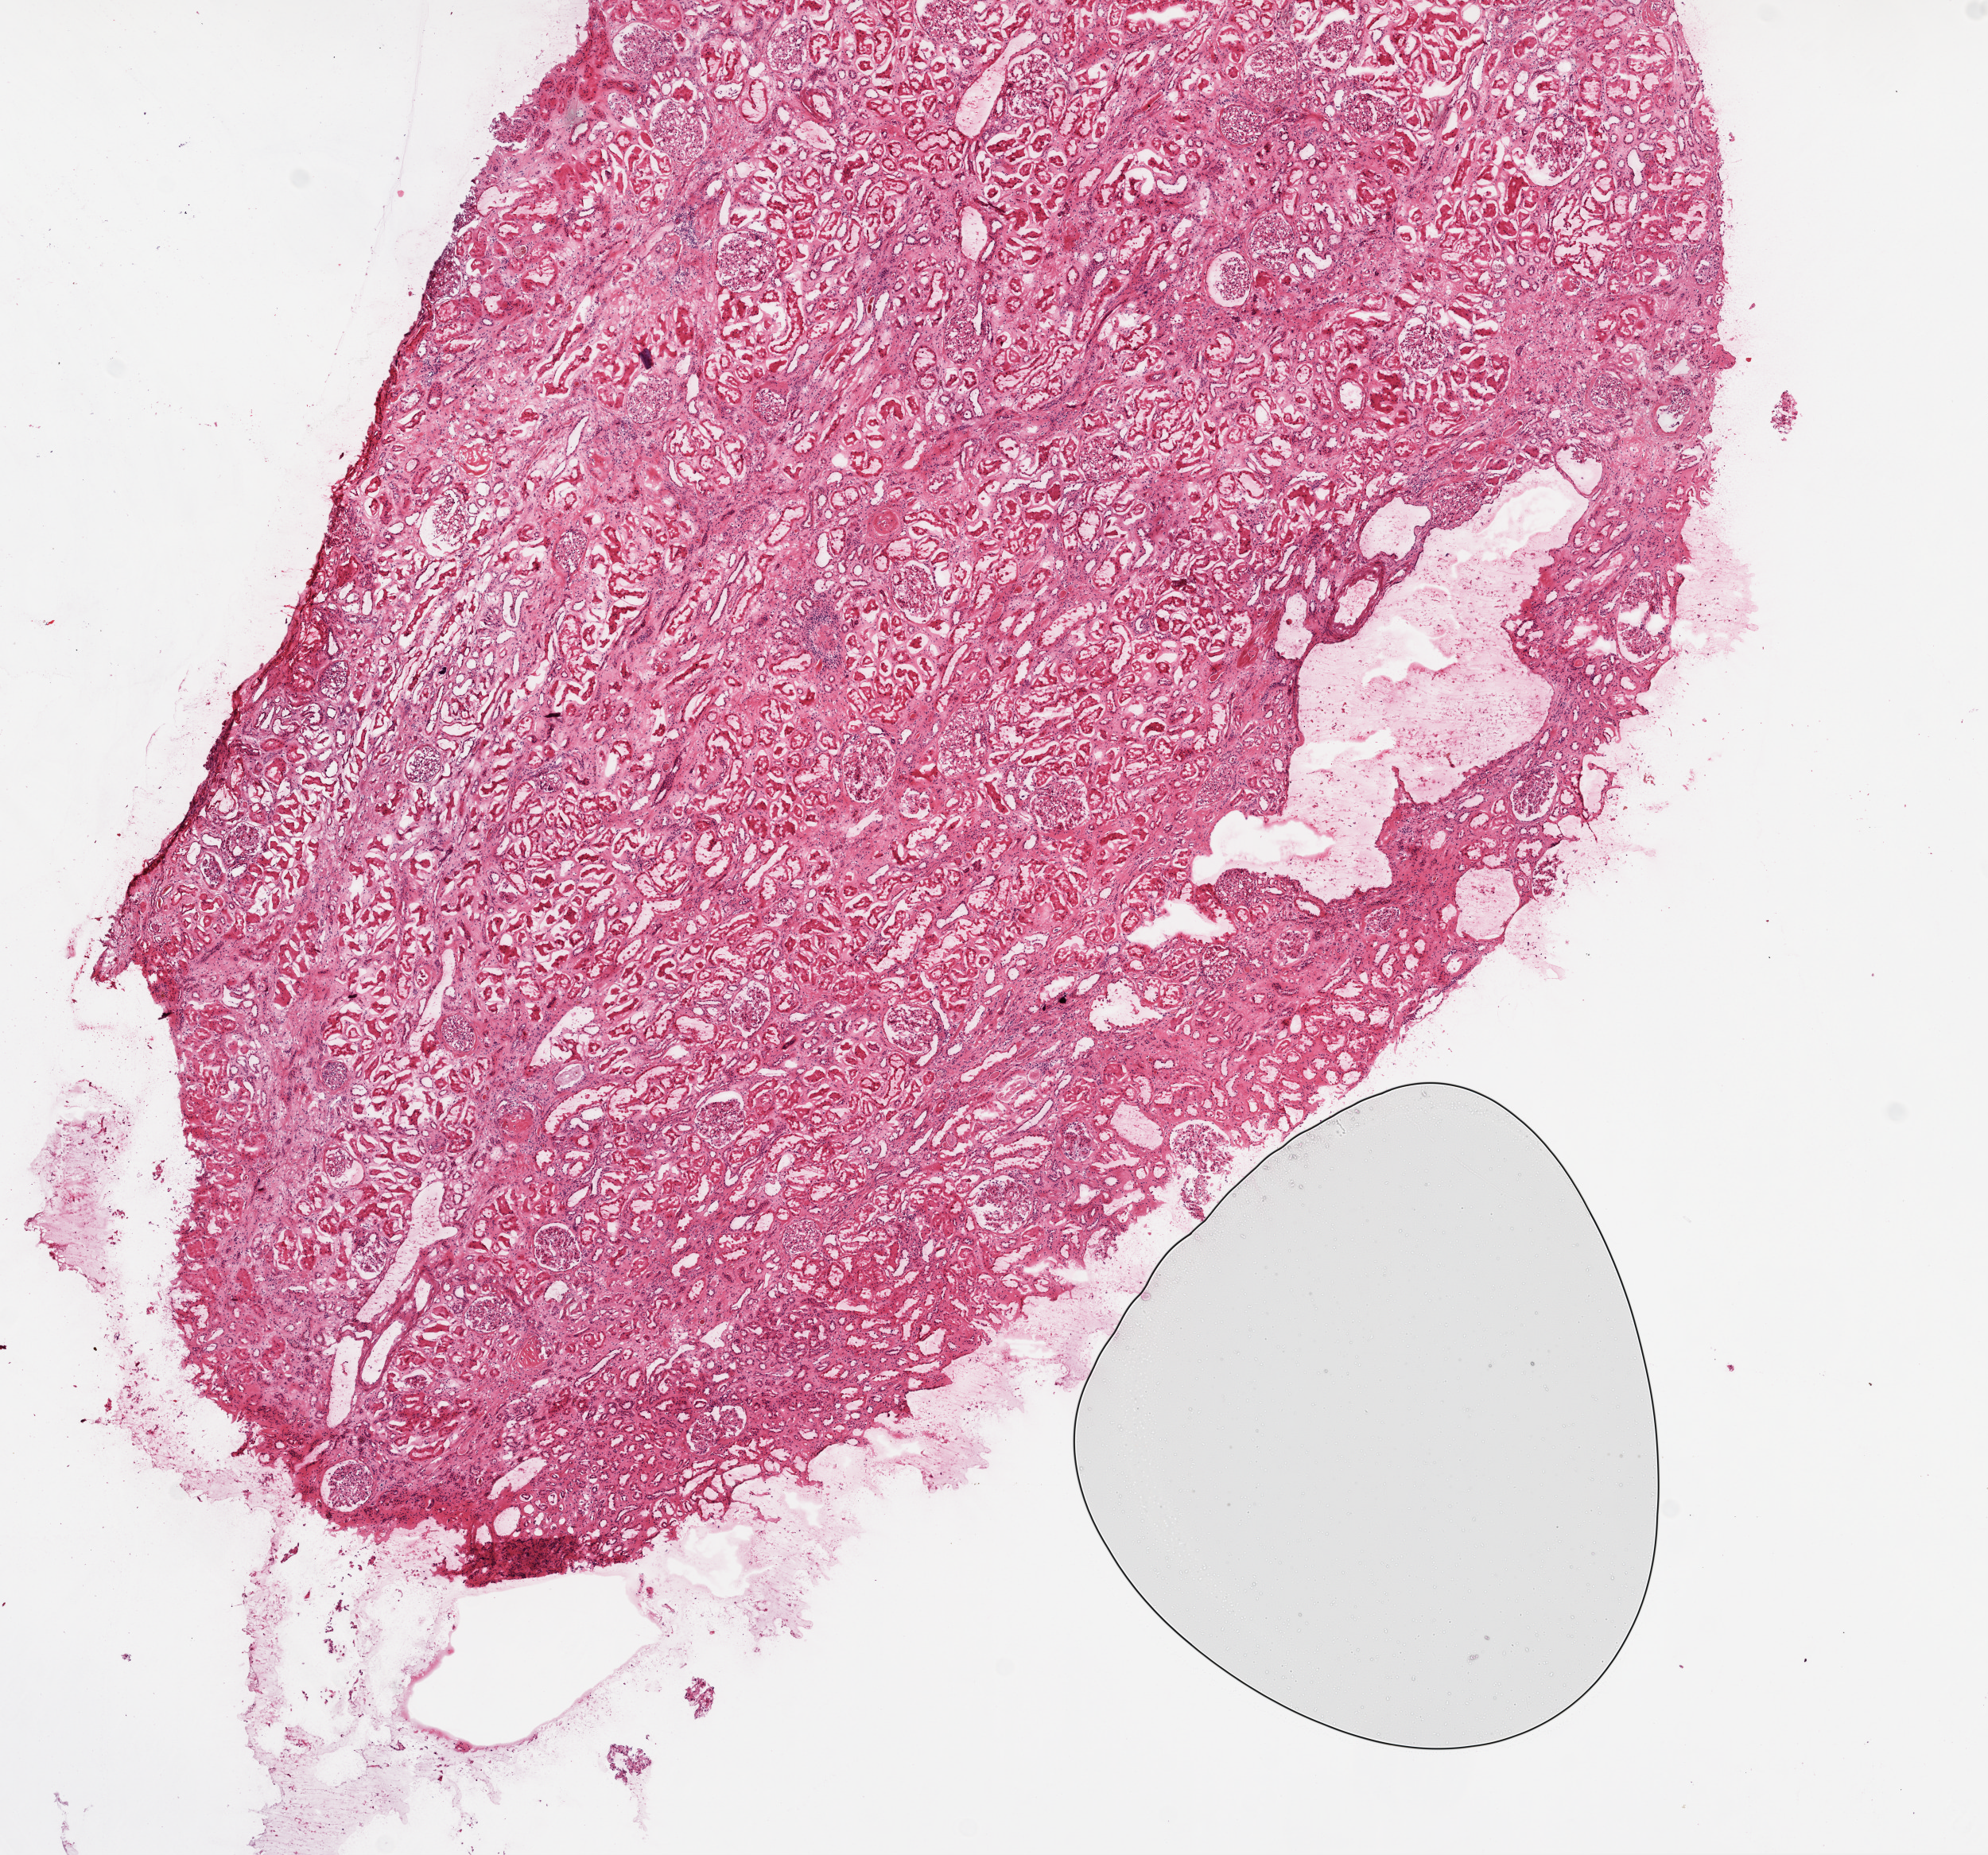
Digitized H&E-stained tissue section (whole slide) — a low-resolution overview of the entire scanned area, about 10.0 x 9.4 mm; frozen section; sample: solid tissue normal (non-tumour tissue), kidney. Male, age 71 years at initial diagnosis.
This section: solid tissue normal sample (biorepository sample class). Patient diagnosis: Clear cell adenocarcinoma, NOS.